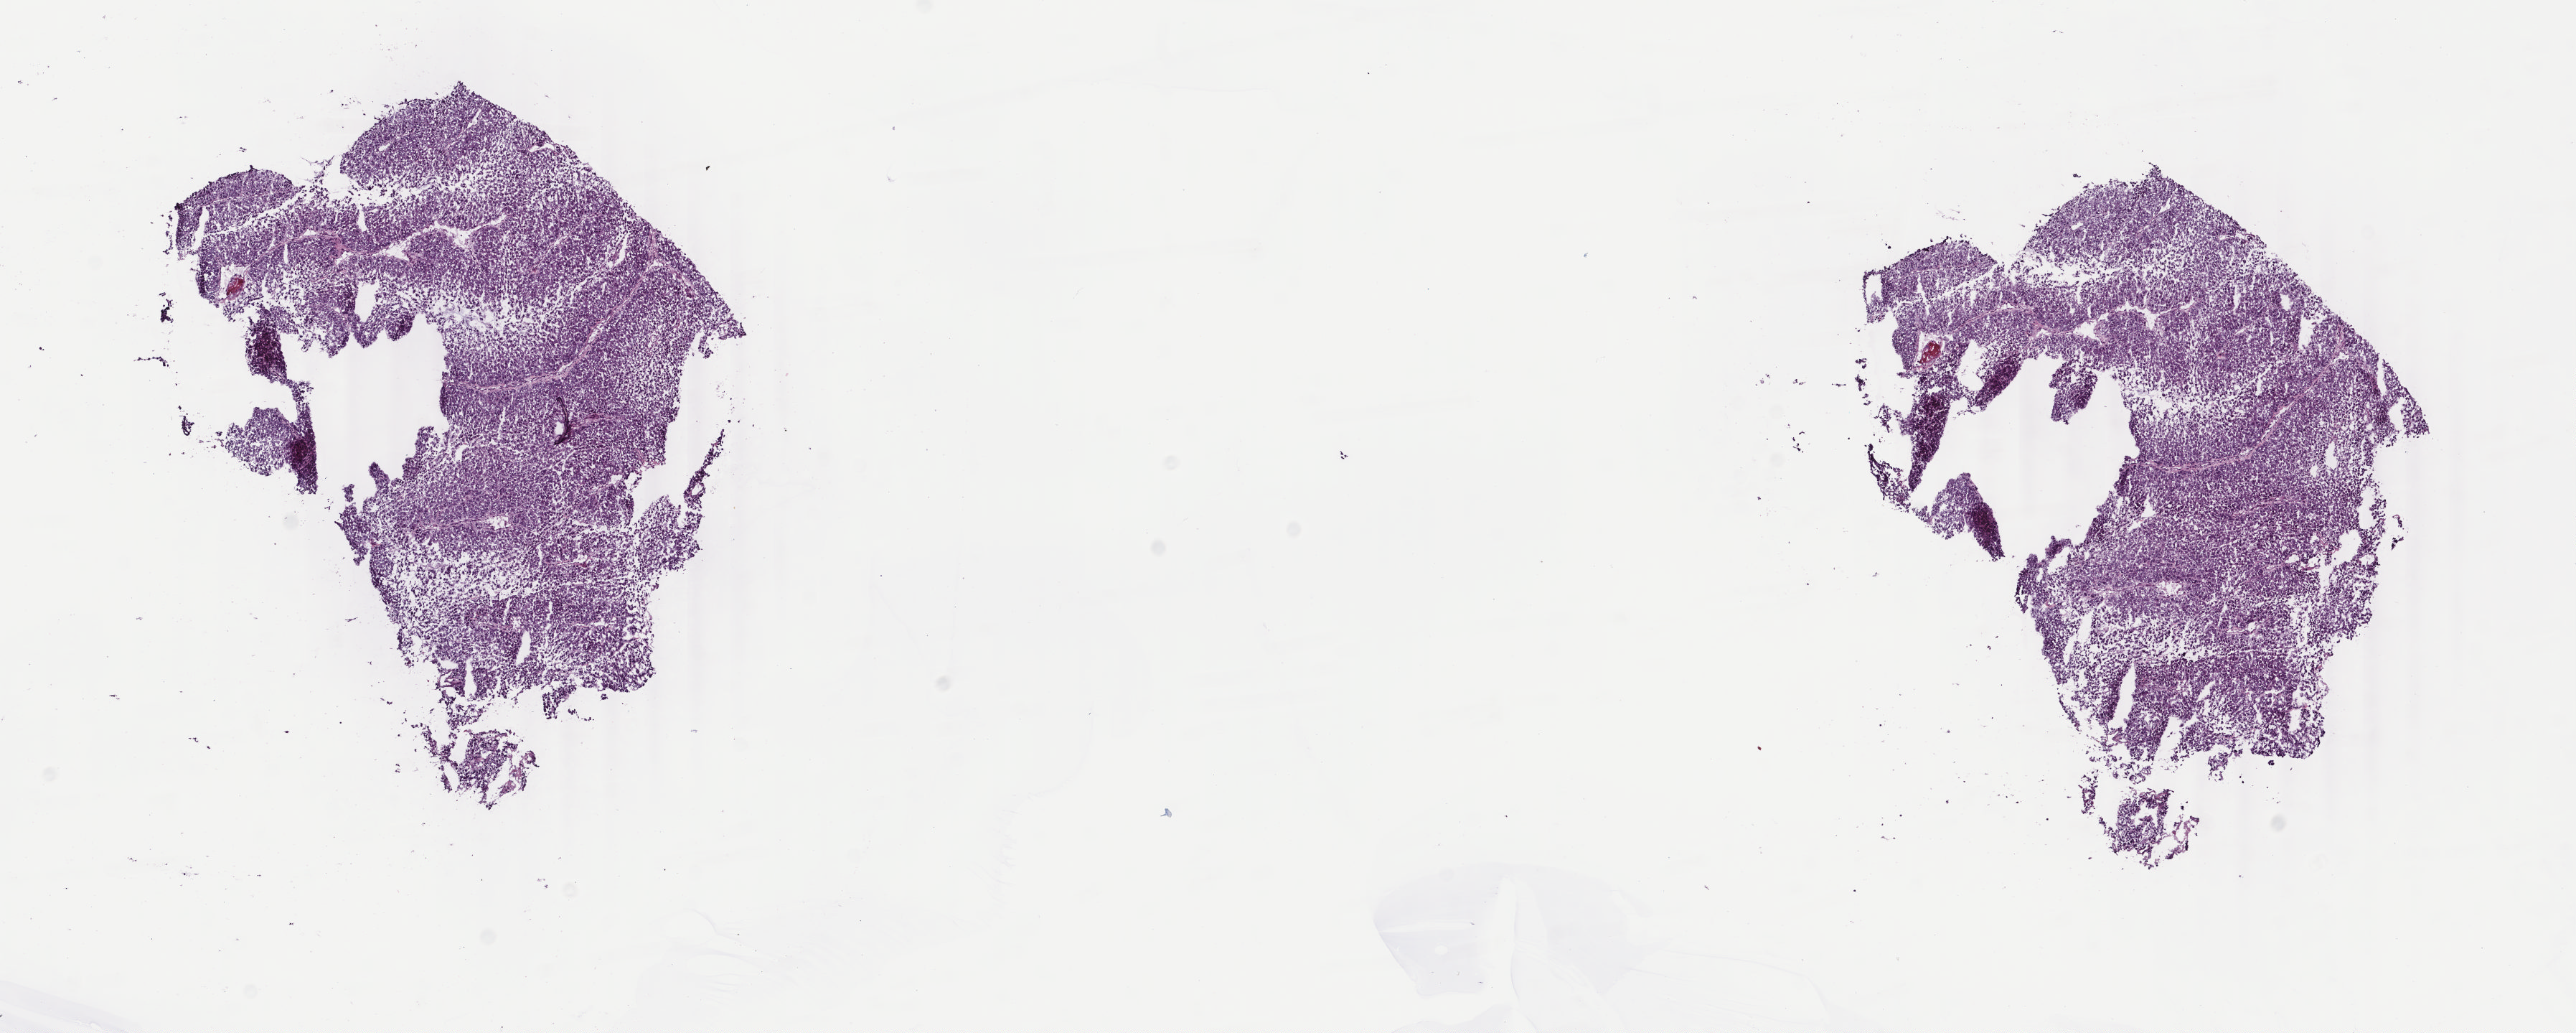
Hematoxylin and eosin (H&E) stained whole-slide image, low-resolution overview of the scanned area, about 14.3 x 5.7 mm (slide scanned at 40x), frozen section from the top of the tissue portion, sample: primary tumour, adrenal cortex. Patient: female, age at initial diagnosis 61 years. Composition of this section per pathologist review: tumour cells 100%, tumour nuclei 95%, normal cells 0%, stromal cells 0%, necrosis 0%. Inflammatory infiltration, as recorded: lymphocyte infiltration 0%, monocyte infiltration 0%, neutrophil infiltration 0%.
* pathologic diagnosis: Adrenal cortical carcinoma (cortex of adrenal gland)